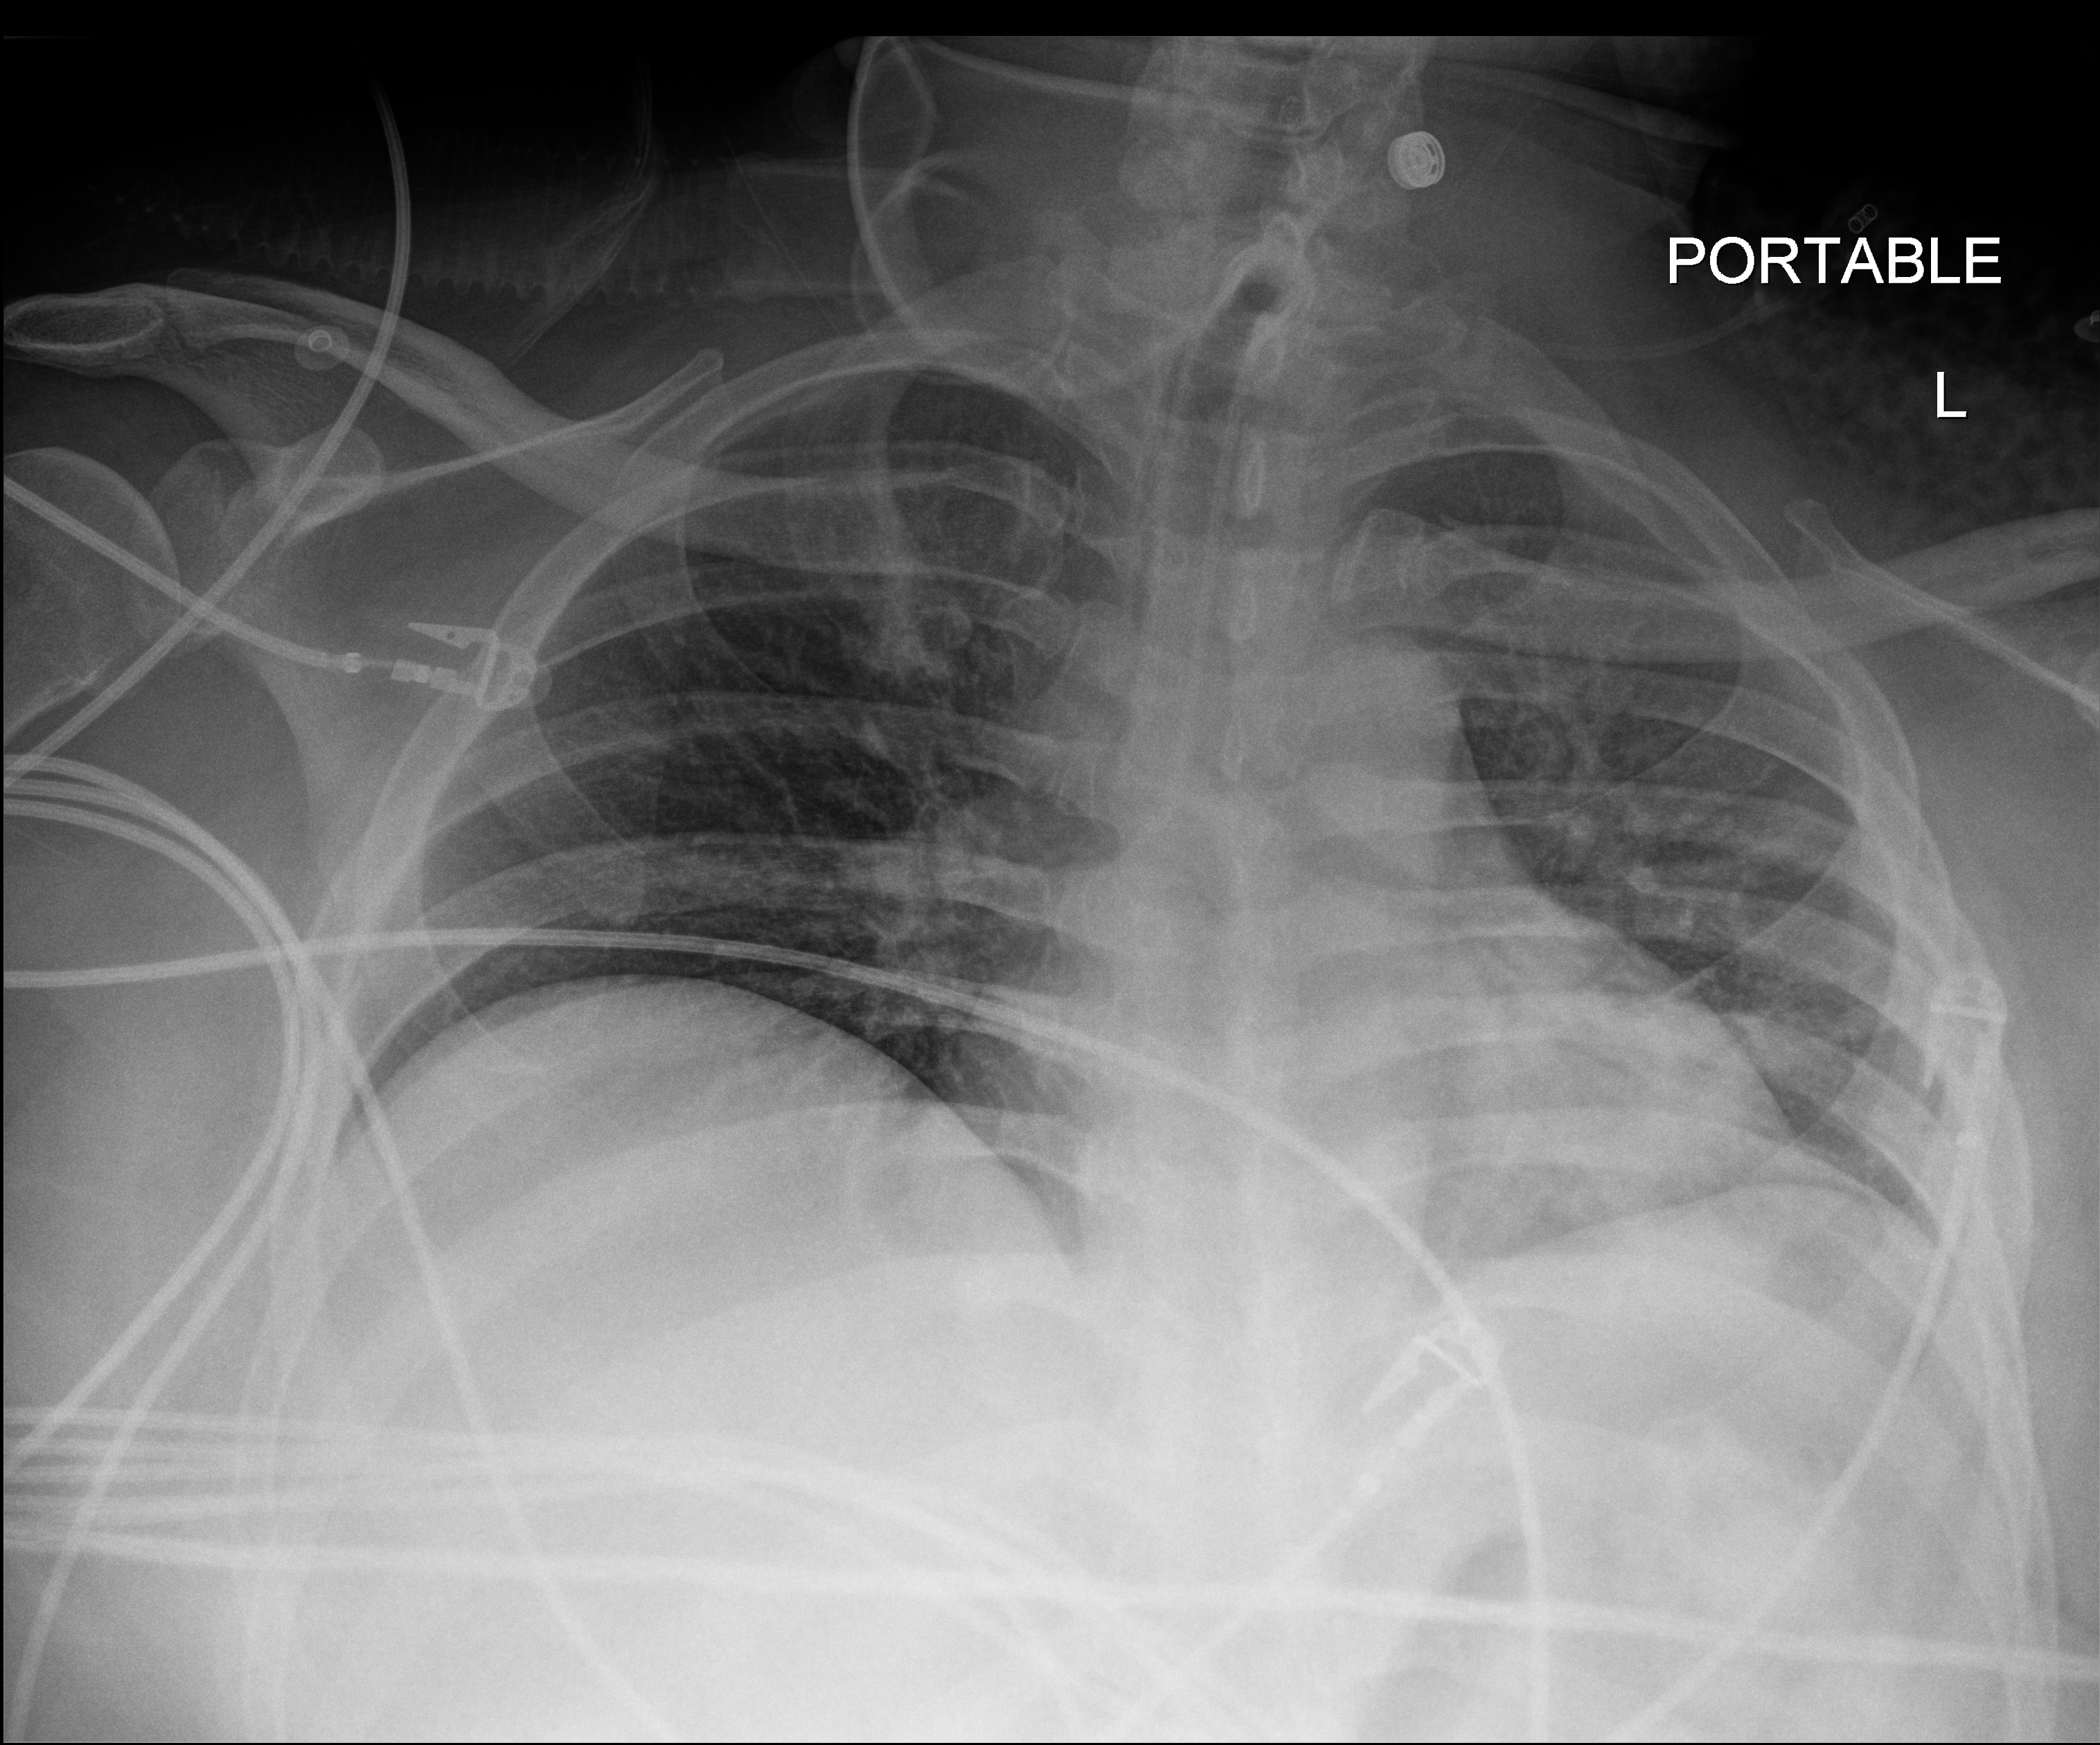
Portable chest radiograph, anteroposterior (AP) projection. Patient hospitalised with COVID-19; male, aged 18–59 years.
Admission-level facts for this patient (not findings on this image; timing relative to this image not recorded): other chronic lung disease (admission record): yes.